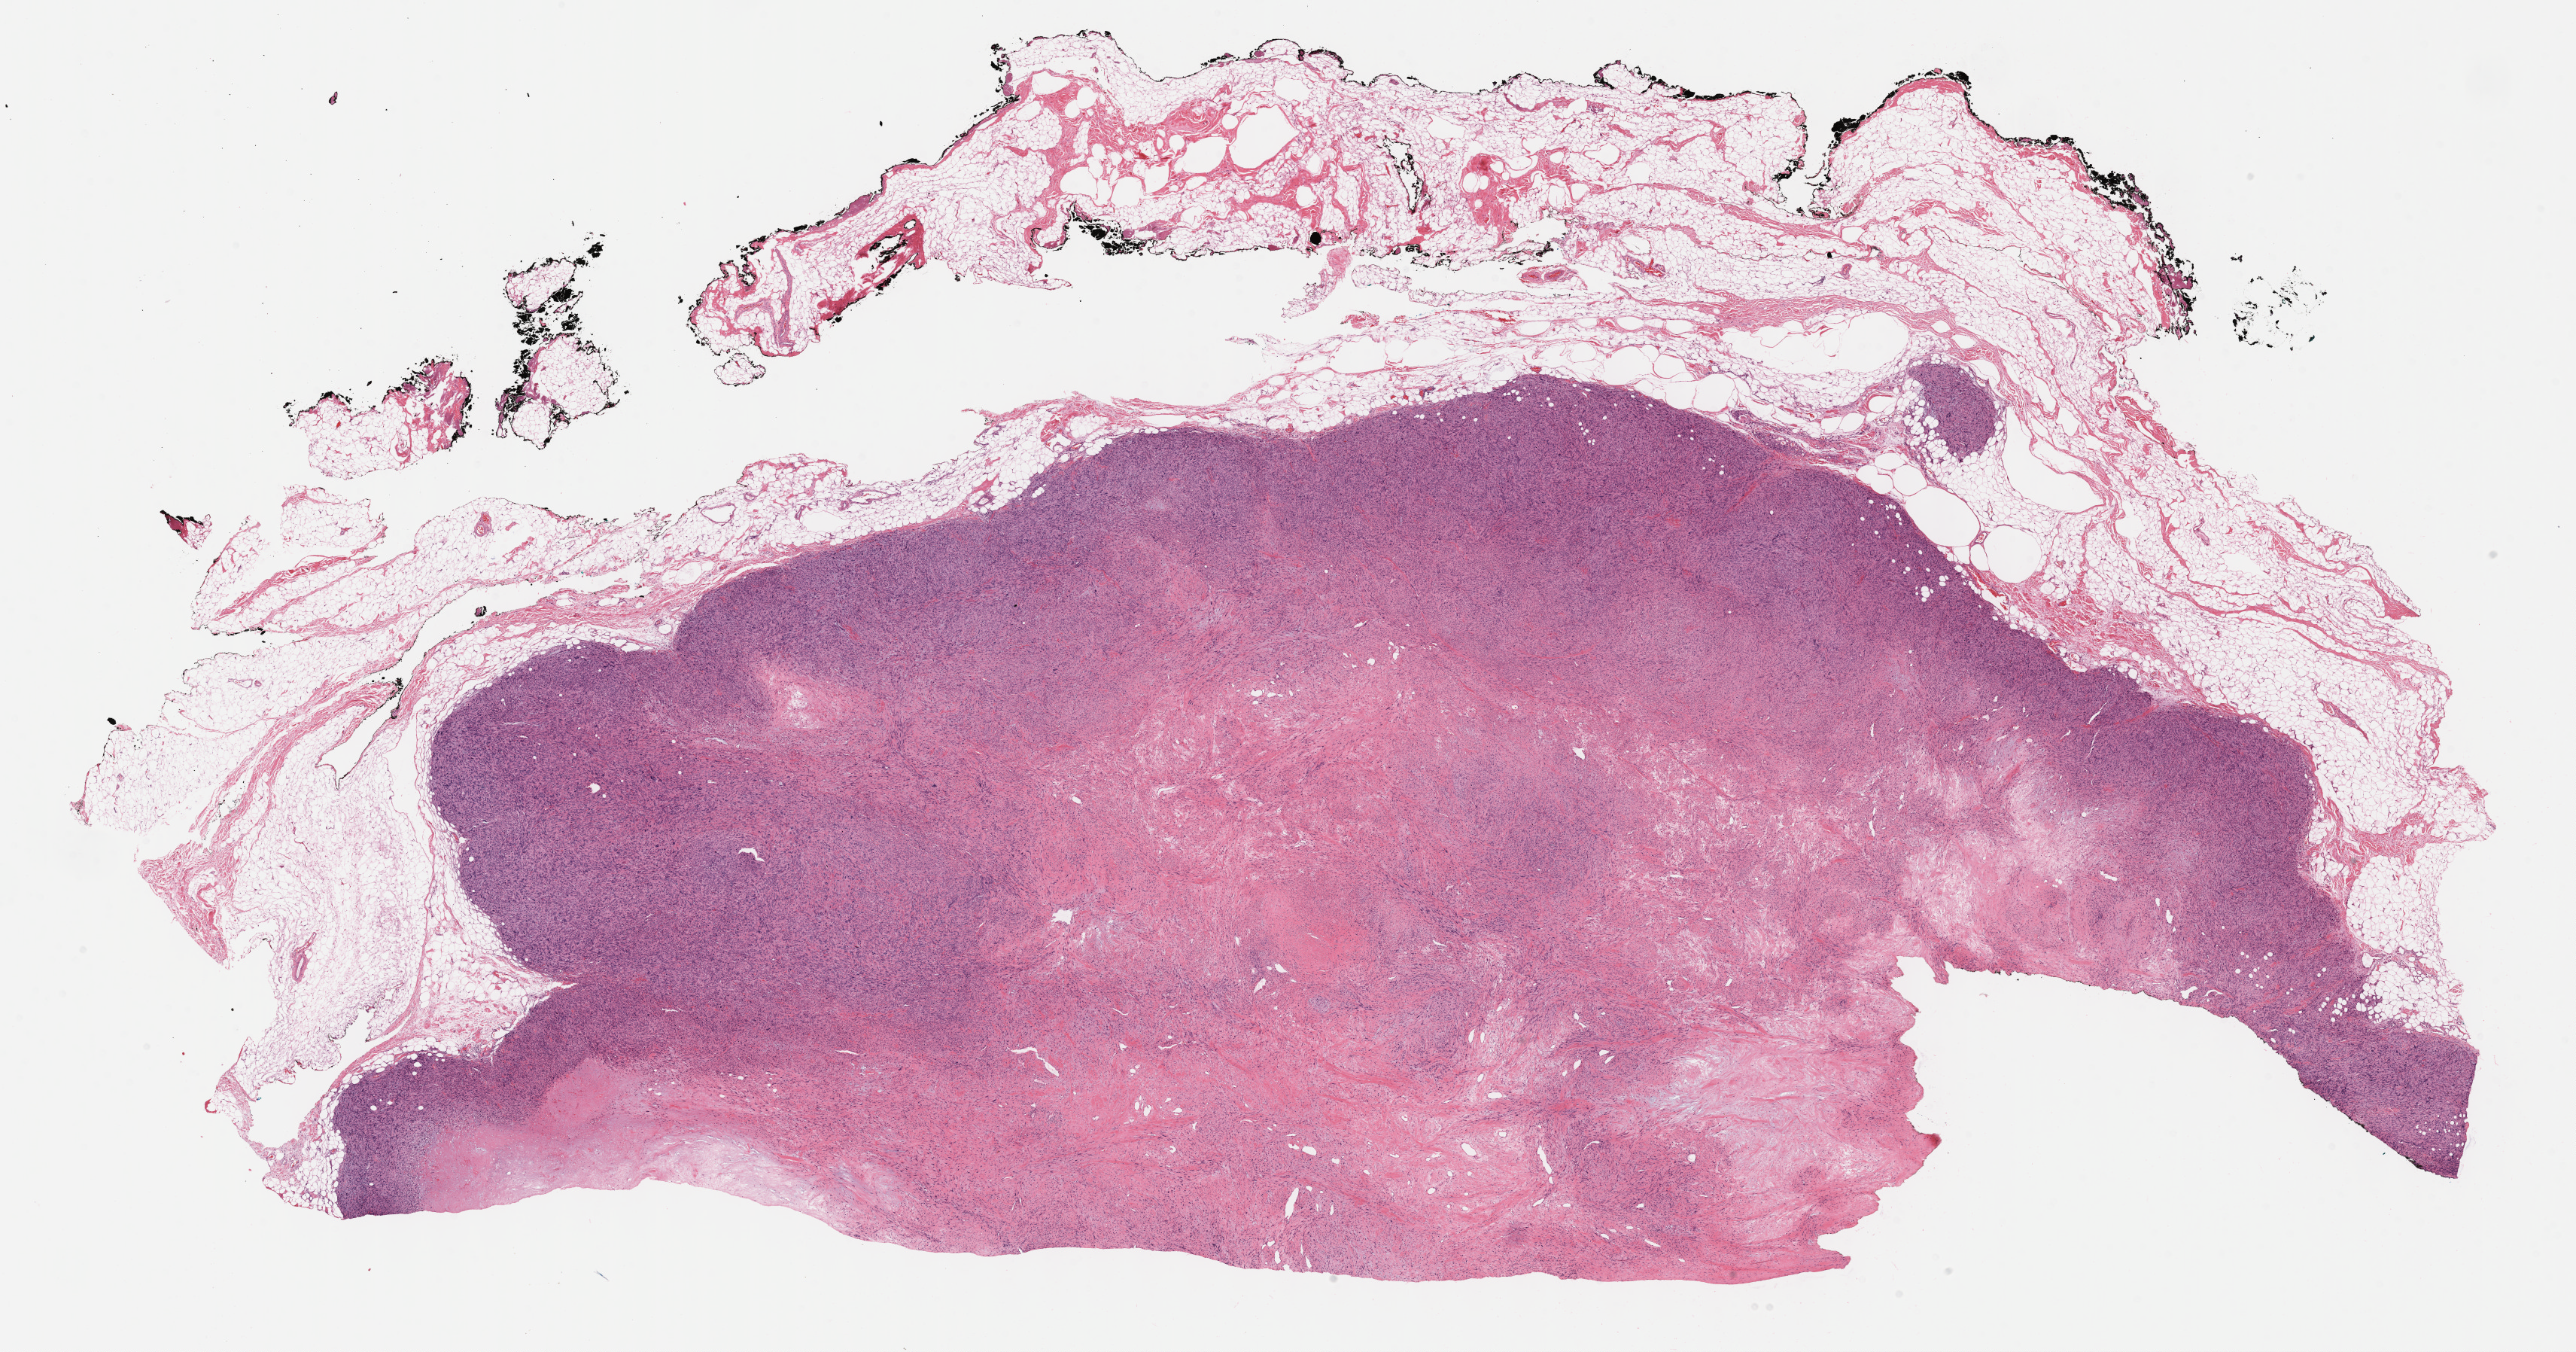
Whole-slide histology image, H&E — a low-resolution overview of the entire scanned area, about 27.7 x 14.5 mm; formalin-fixed paraffin-embedded (FFPE) diagnostic section; connective, subcutaneous and other soft tissues, primary tumour sample. Female, age 52 years at initial diagnosis.
- diagnosis: Leiomyosarcoma, NOS (connective, subcutaneous and other soft tissues of upper limb and shoulder)